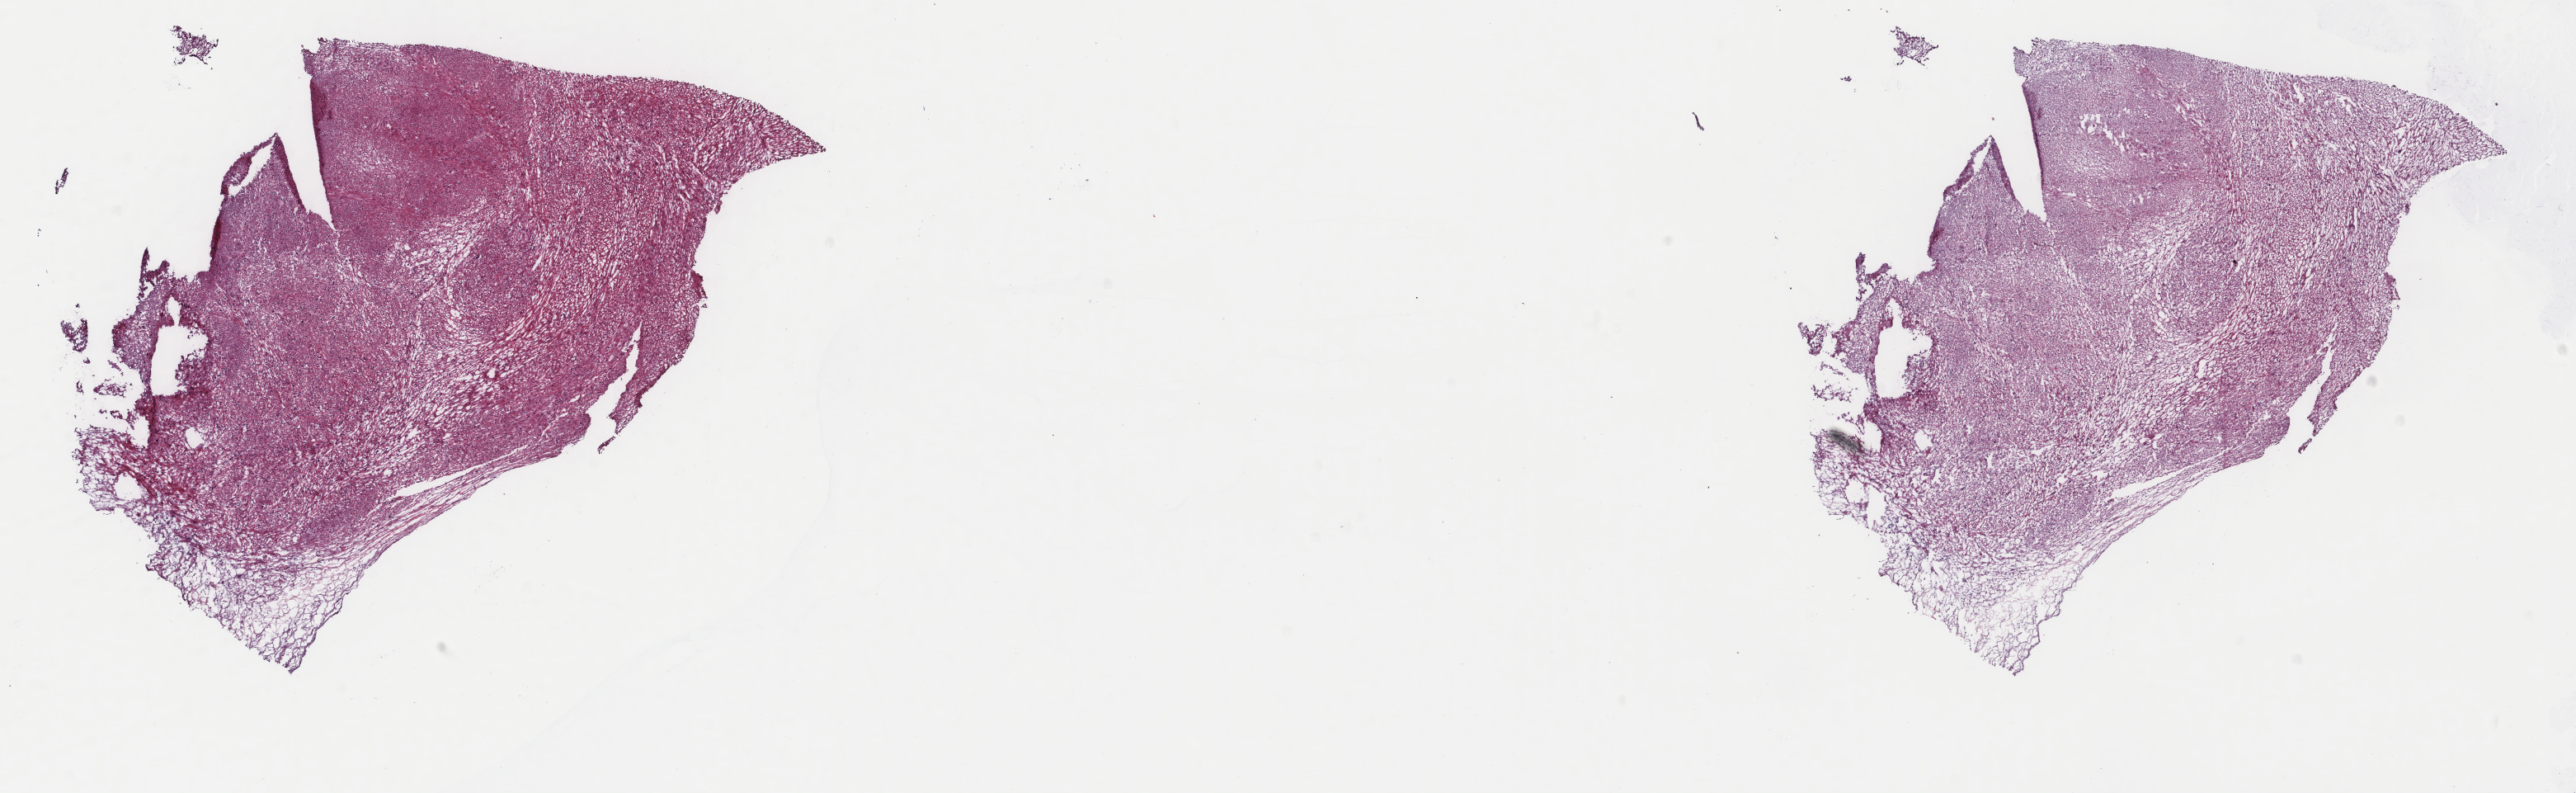
H&E whole-slide image, low-resolution overview of the scanned area, about 24.8 x 7.6 mm (acquisition: 40x scan), frozen section, primary tumour sample from the retroperitoneum and peritoneum. Patient: male, age at initial diagnosis 55 years. Composition of this section per pathologist review: tumour cells 95%, tumour nuclei 95%, normal cells 0%, stromal cells 5%, necrosis 0%. Inflammatory infiltration, as recorded: lymphocyte infiltration 0%, monocyte infiltration 0%, neutrophil infiltration 0%.
Histologic diagnosis: Leiomyosarcoma, NOS.